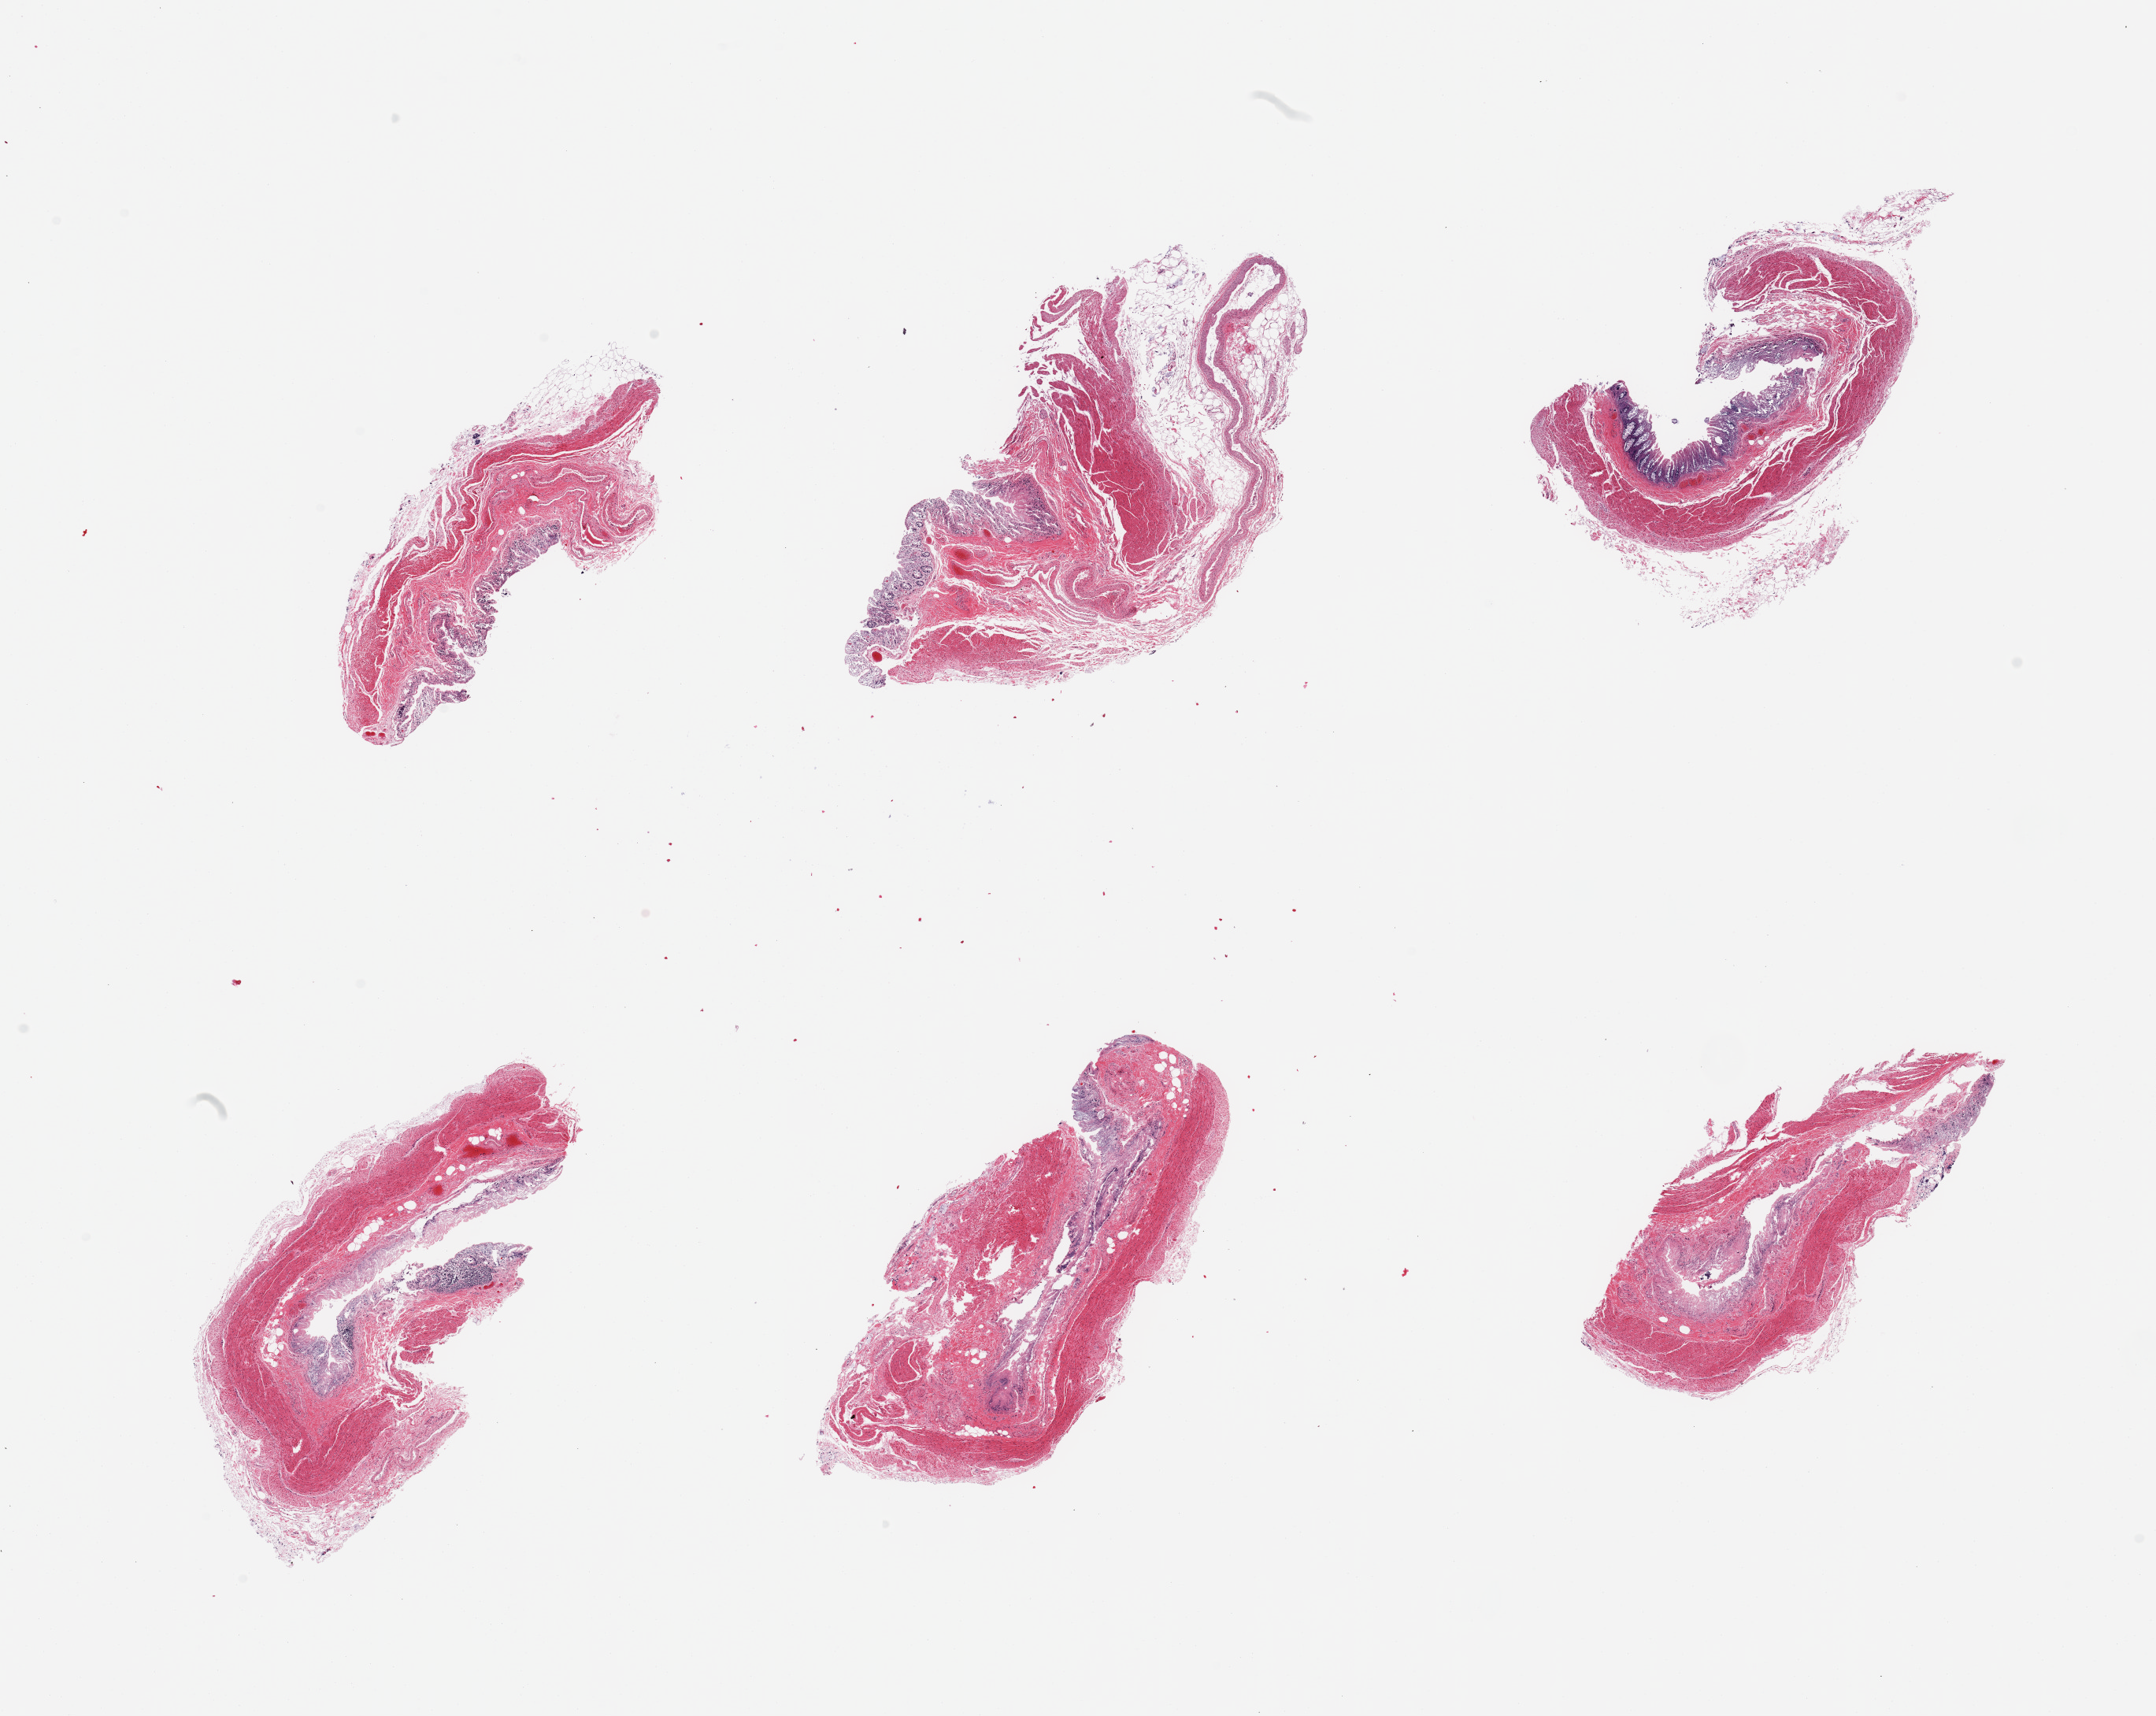
Whole-slide image, hematoxylin and eosin (H&E) stain — a low-resolution overview of the entire scanned area, about 21.7 x 17.2 mm, PAXgene-fixed, paraffin-embedded tissue, sampled site (target tissue): transverse colon, tissue donor sample. Donor: male.
Pathologist's review note for this sample: 6 pieces; full thickness, autolyzed.